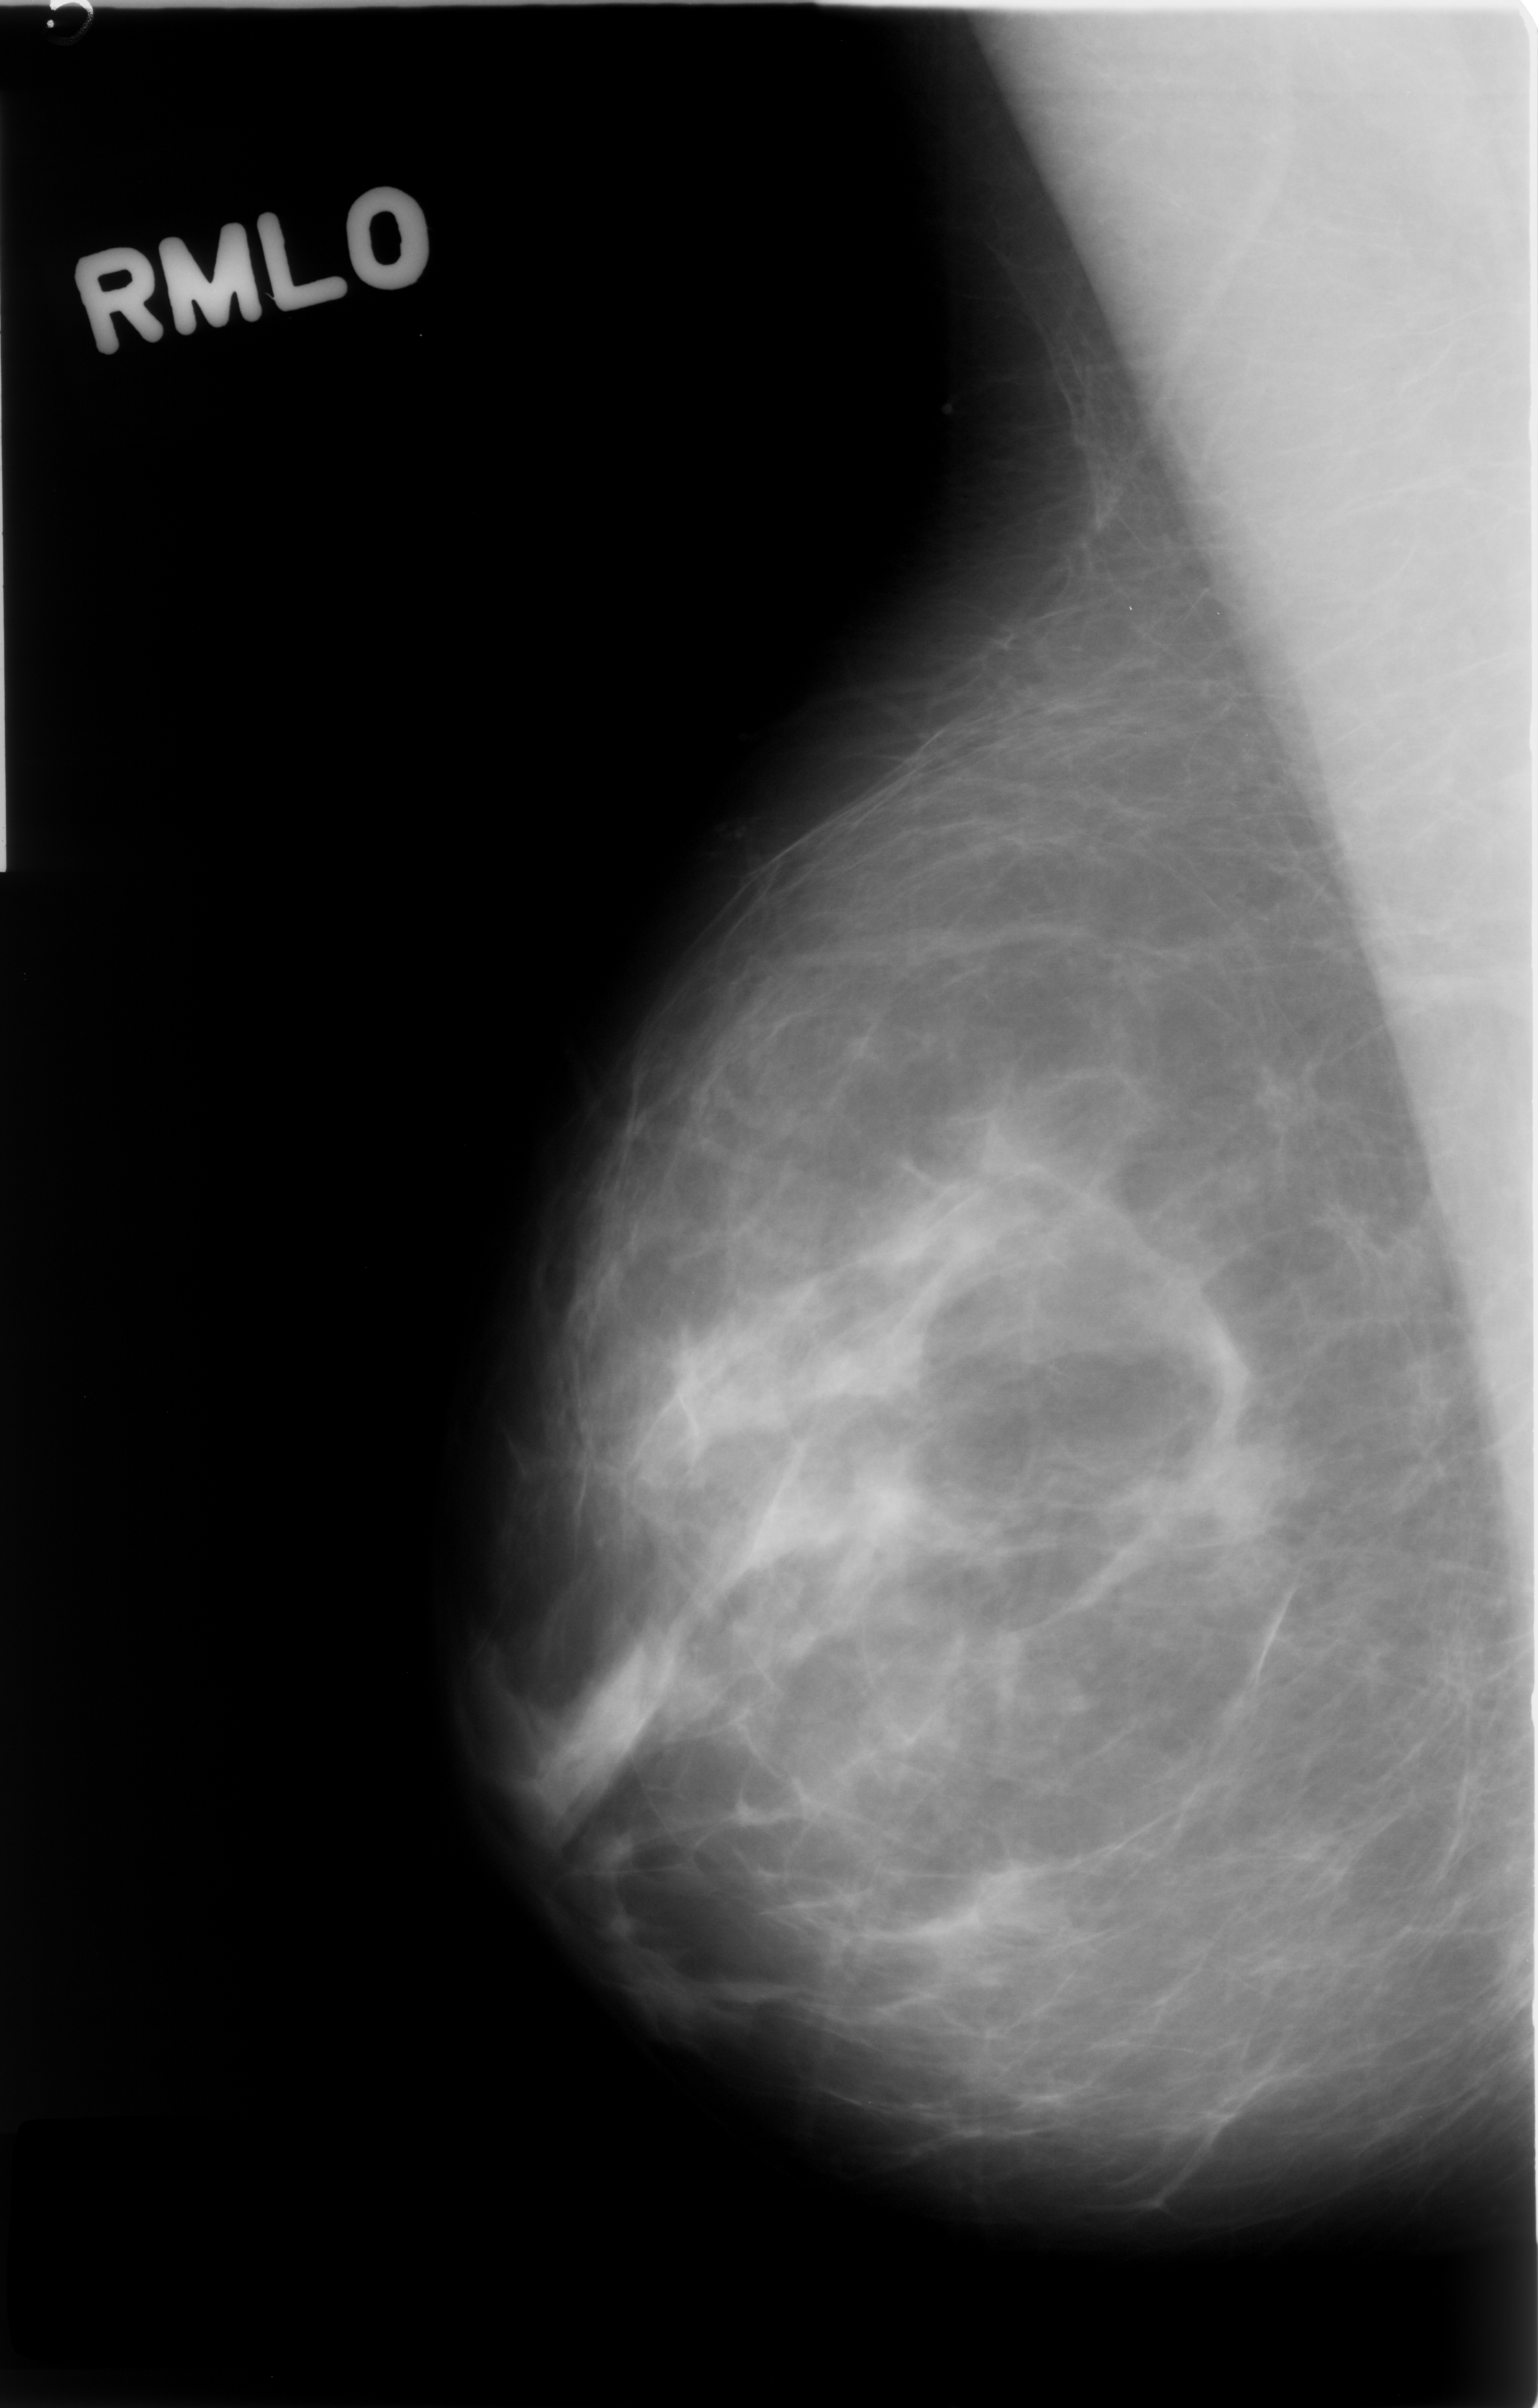
Mammogram (digitized film), right breast, mediolateral oblique (MLO) view.
Abnormality record for this image: mass, shape irregular, margins ill defined; BI-RADS assessment category 3; benign; no additional work-up was recommended (benign without callback).